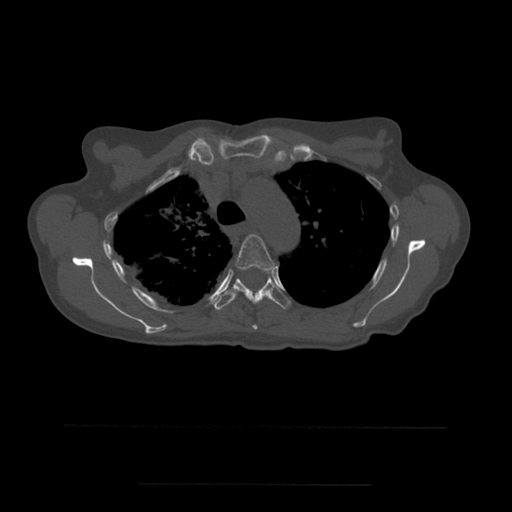
CT including the spine, one axial slice; bone window (W 1800 / L 400 HU); 1.25 mm slice thickness; 512 × 512 image matrix, field of view 350 × 350 mm. Patient age 58 years. Case-level facts recorded for this patient, not image findings: primary cancer: lung.
Annotated regions visible in this slice (semi-automatically segmented with operator editing):
- T4 vertebra: box from (x=235, y=234) to (x=275, y=330) px
- T5 vertebra: (x=215, y=273)–(x=290, y=311)